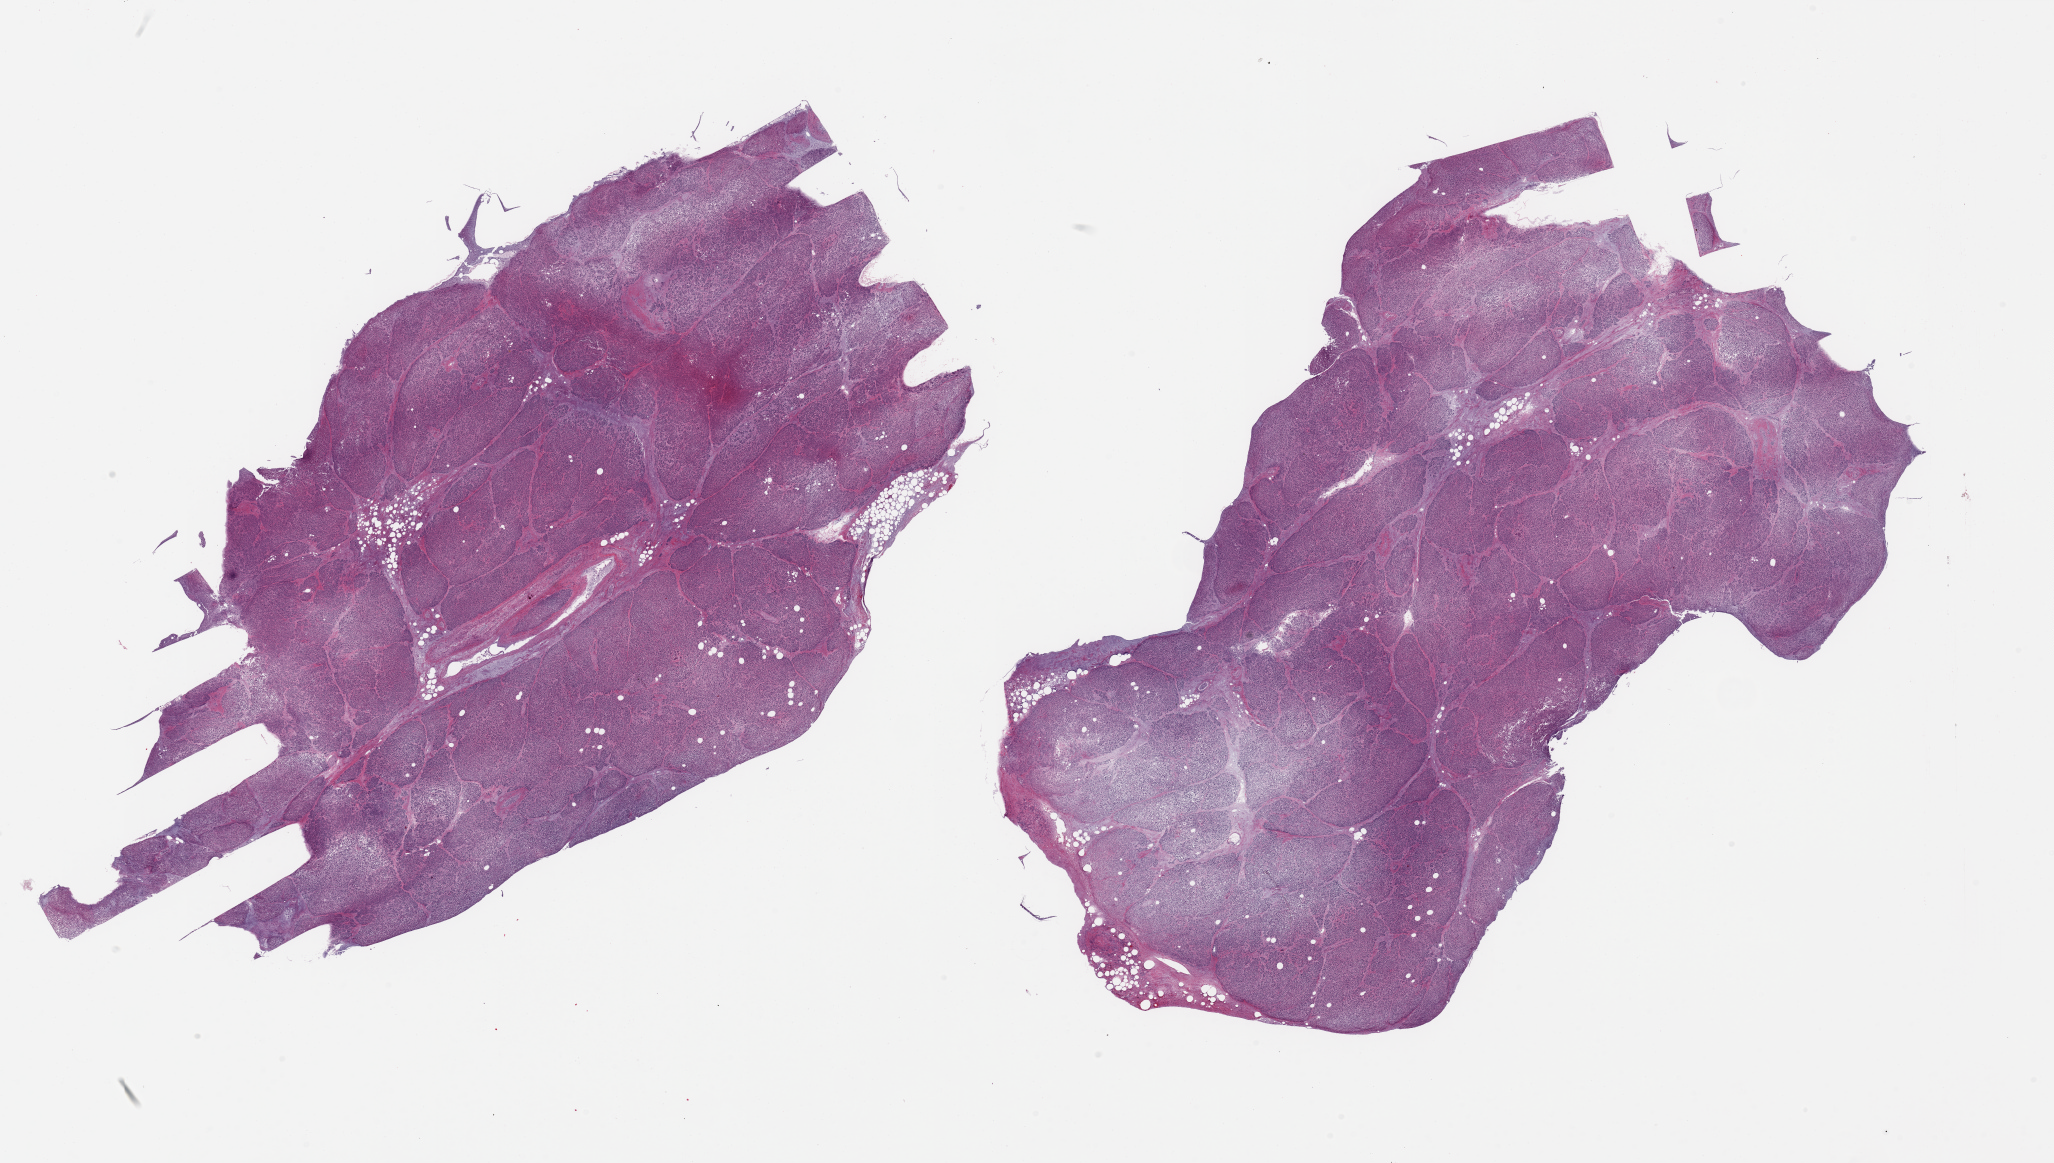
Digitized haematoxylin and eosin-stained section, brightfield — a low-resolution overview of the entire scanned area, about 32.5 x 18.4 mm; PAXgene-fixed paraffin-embedded (PFPE) section; sampled site (target tissue): pancreas; tissue donor sample.
* pathologist's review note for this sample: 2 pieces; severe autolysis; minimal external fat